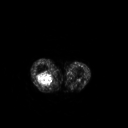
FDG PET of an extremity soft-tissue mass (from a PET/CT study), one axial slice; slice 182 of 267 in the series (ordered by position); 3.27 mm slice thickness; 128 × 128 image matrix. Patient: female, 62 years. From the clinical record (not read from this slice): histological type: liposarcoma; site of the primary tumour: right thigh.
Outlined on this slice (expert contour drawn on MRI and transferred to this co-registered scan by the dataset authors):
- gross tumour volume (mass): box from (x=36, y=72) to (x=54, y=88) px